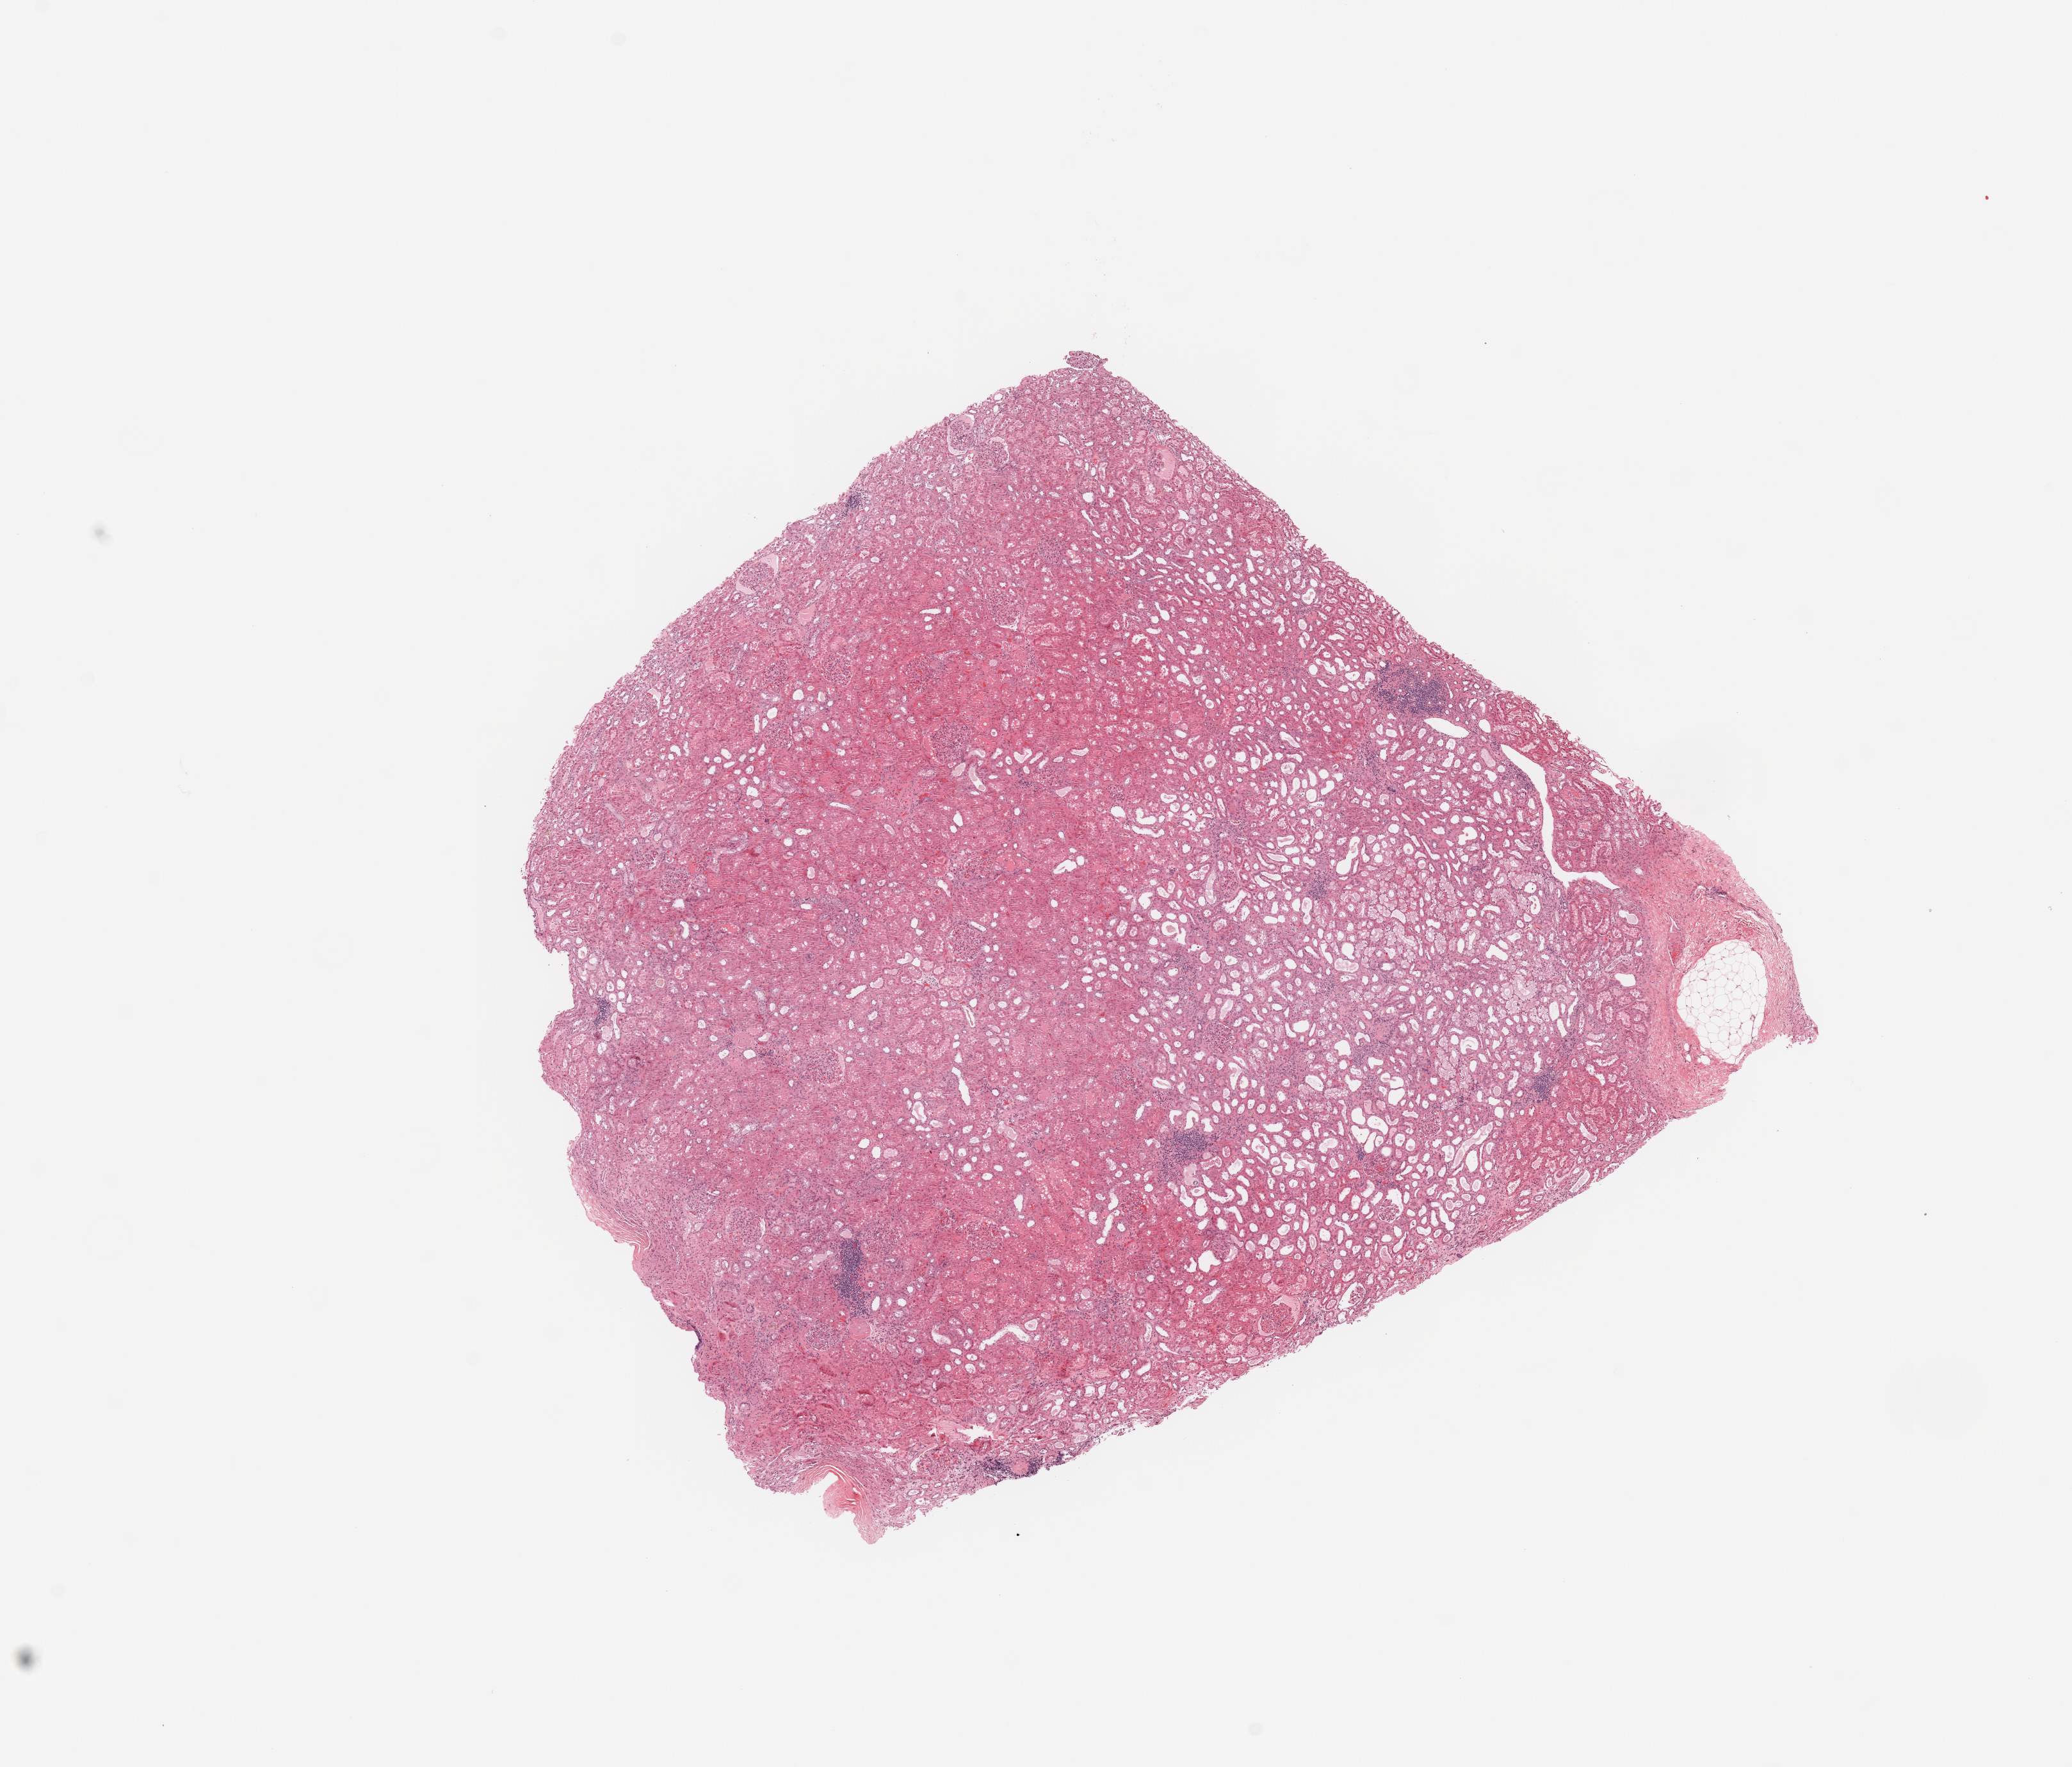
Digitized Hematoxylin and eosin (H&E) stained tissue section (whole slide), shown as a low-resolution overview of the whole scanned area (about 12.8 x 10.9 mm), normal (non-tumour) tissue sample, sampled site: kidney. Patient: male, age 60 years.
This section: normal (non-tumour) tissue from the same patient. Patient diagnosis: Renal cell carcinoma, NOS.